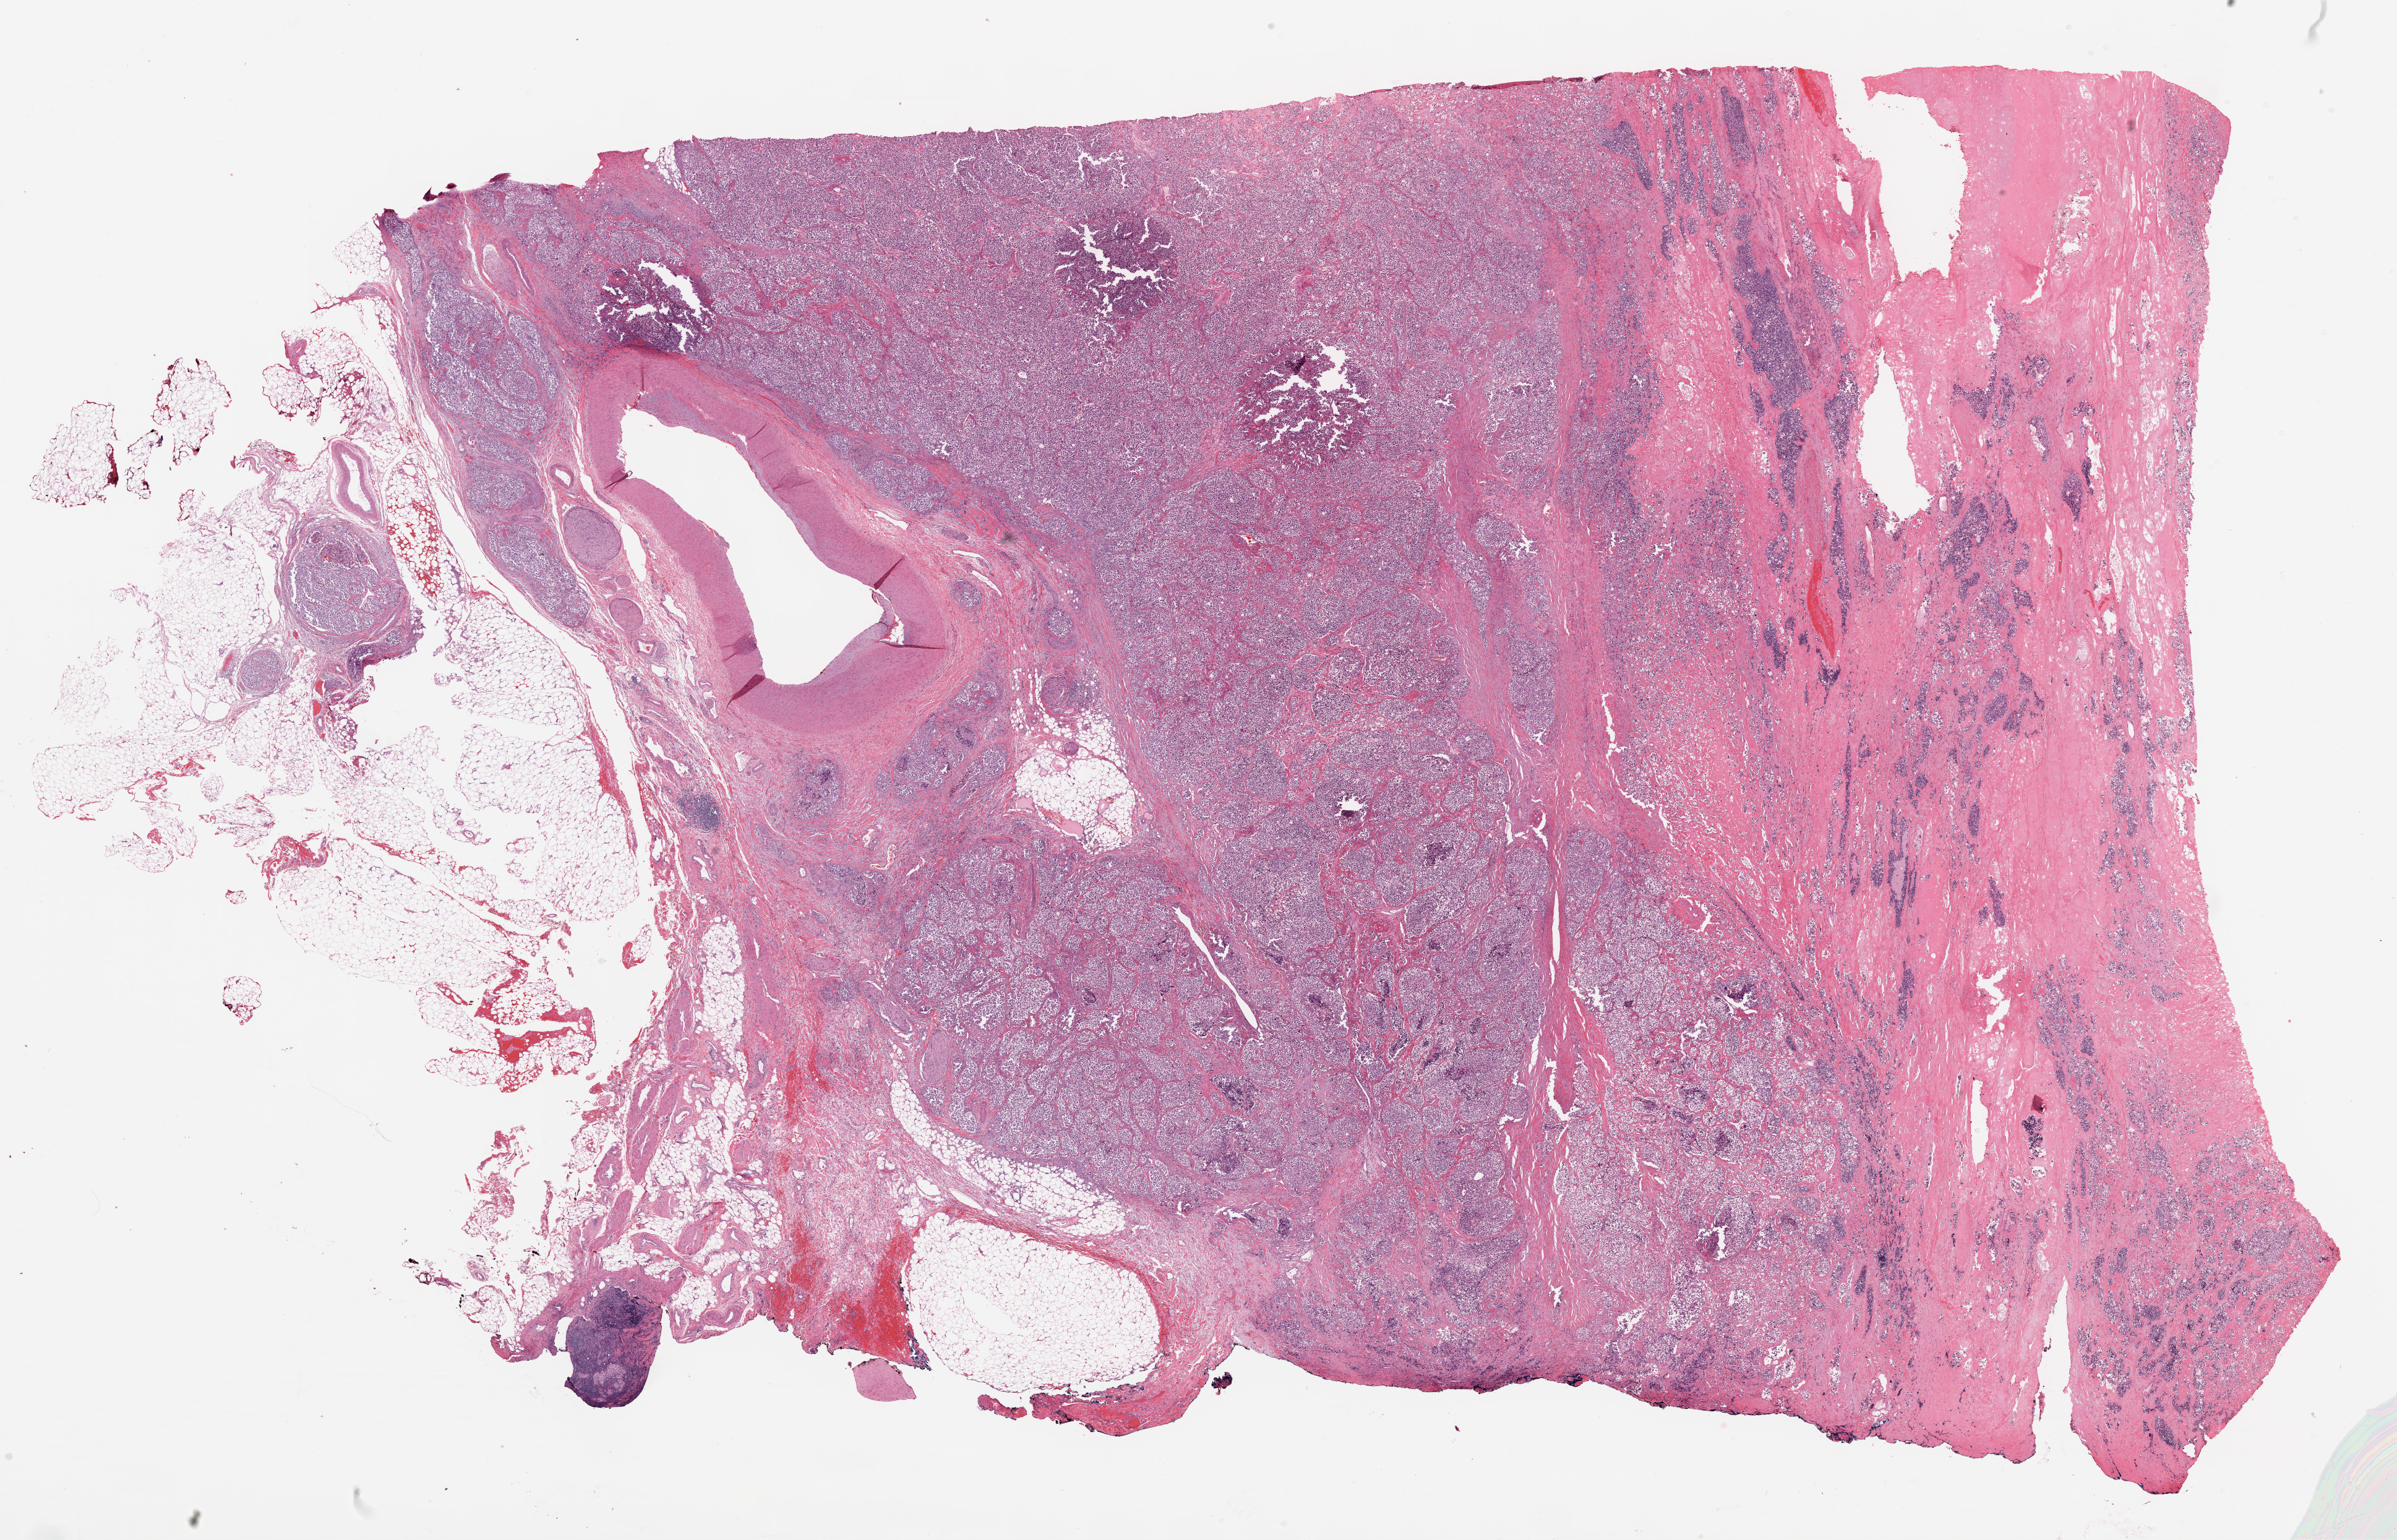
Whole-slide histology image, H&E-stained — low-resolution overview of the scanned area, about 31.1 x 20.0 mm (slide scanned at 20x), formalin-fixed paraffin-embedded (FFPE) diagnostic section, sample: primary tumour, kidney. Male, age 60 years at initial diagnosis. Histologic grade: G4 (undifferentiated).
Laterality: right. AJCC pathologic stage: IV. Pathologic diagnosis: Clear cell adenocarcinoma, NOS.